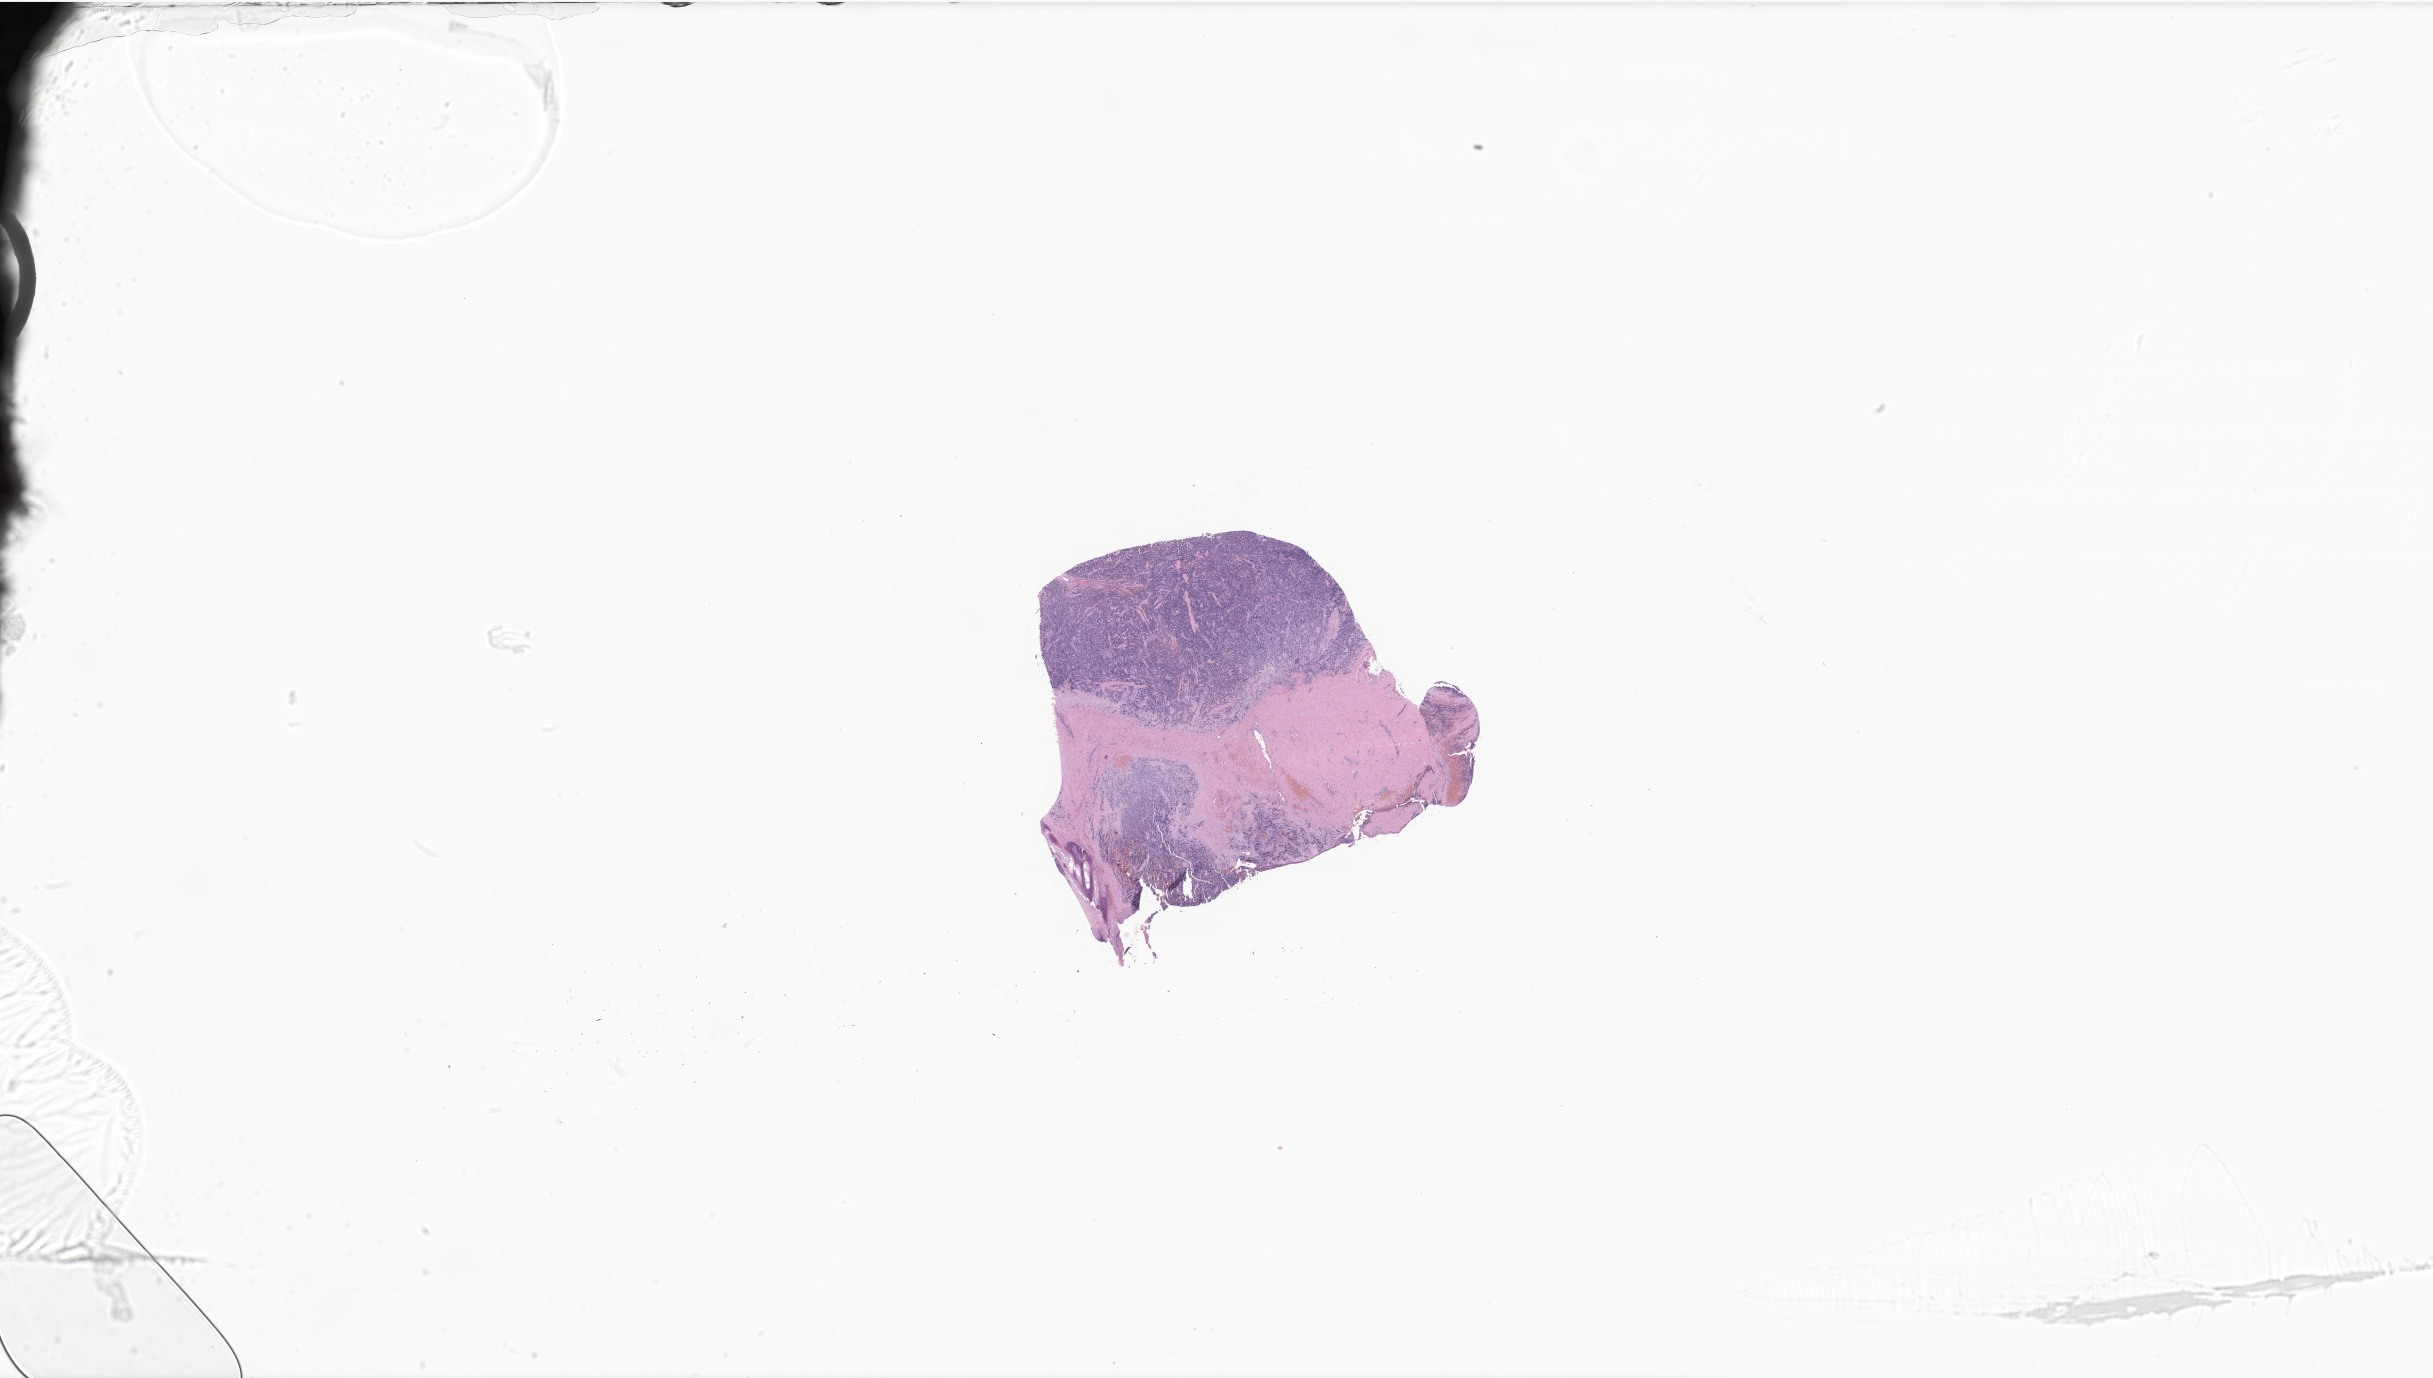
Digitized haematoxylin and eosin-stained section of tumor tissue from the nasal cavity, a low-resolution overview of the entire scanned area, about 41.0 x 23.2 mm; FFPE section. Patient: female, age 128 months (10 years 8 months).
• recorded diagnosis: Embryonal rhabdomyosarcoma, NOS